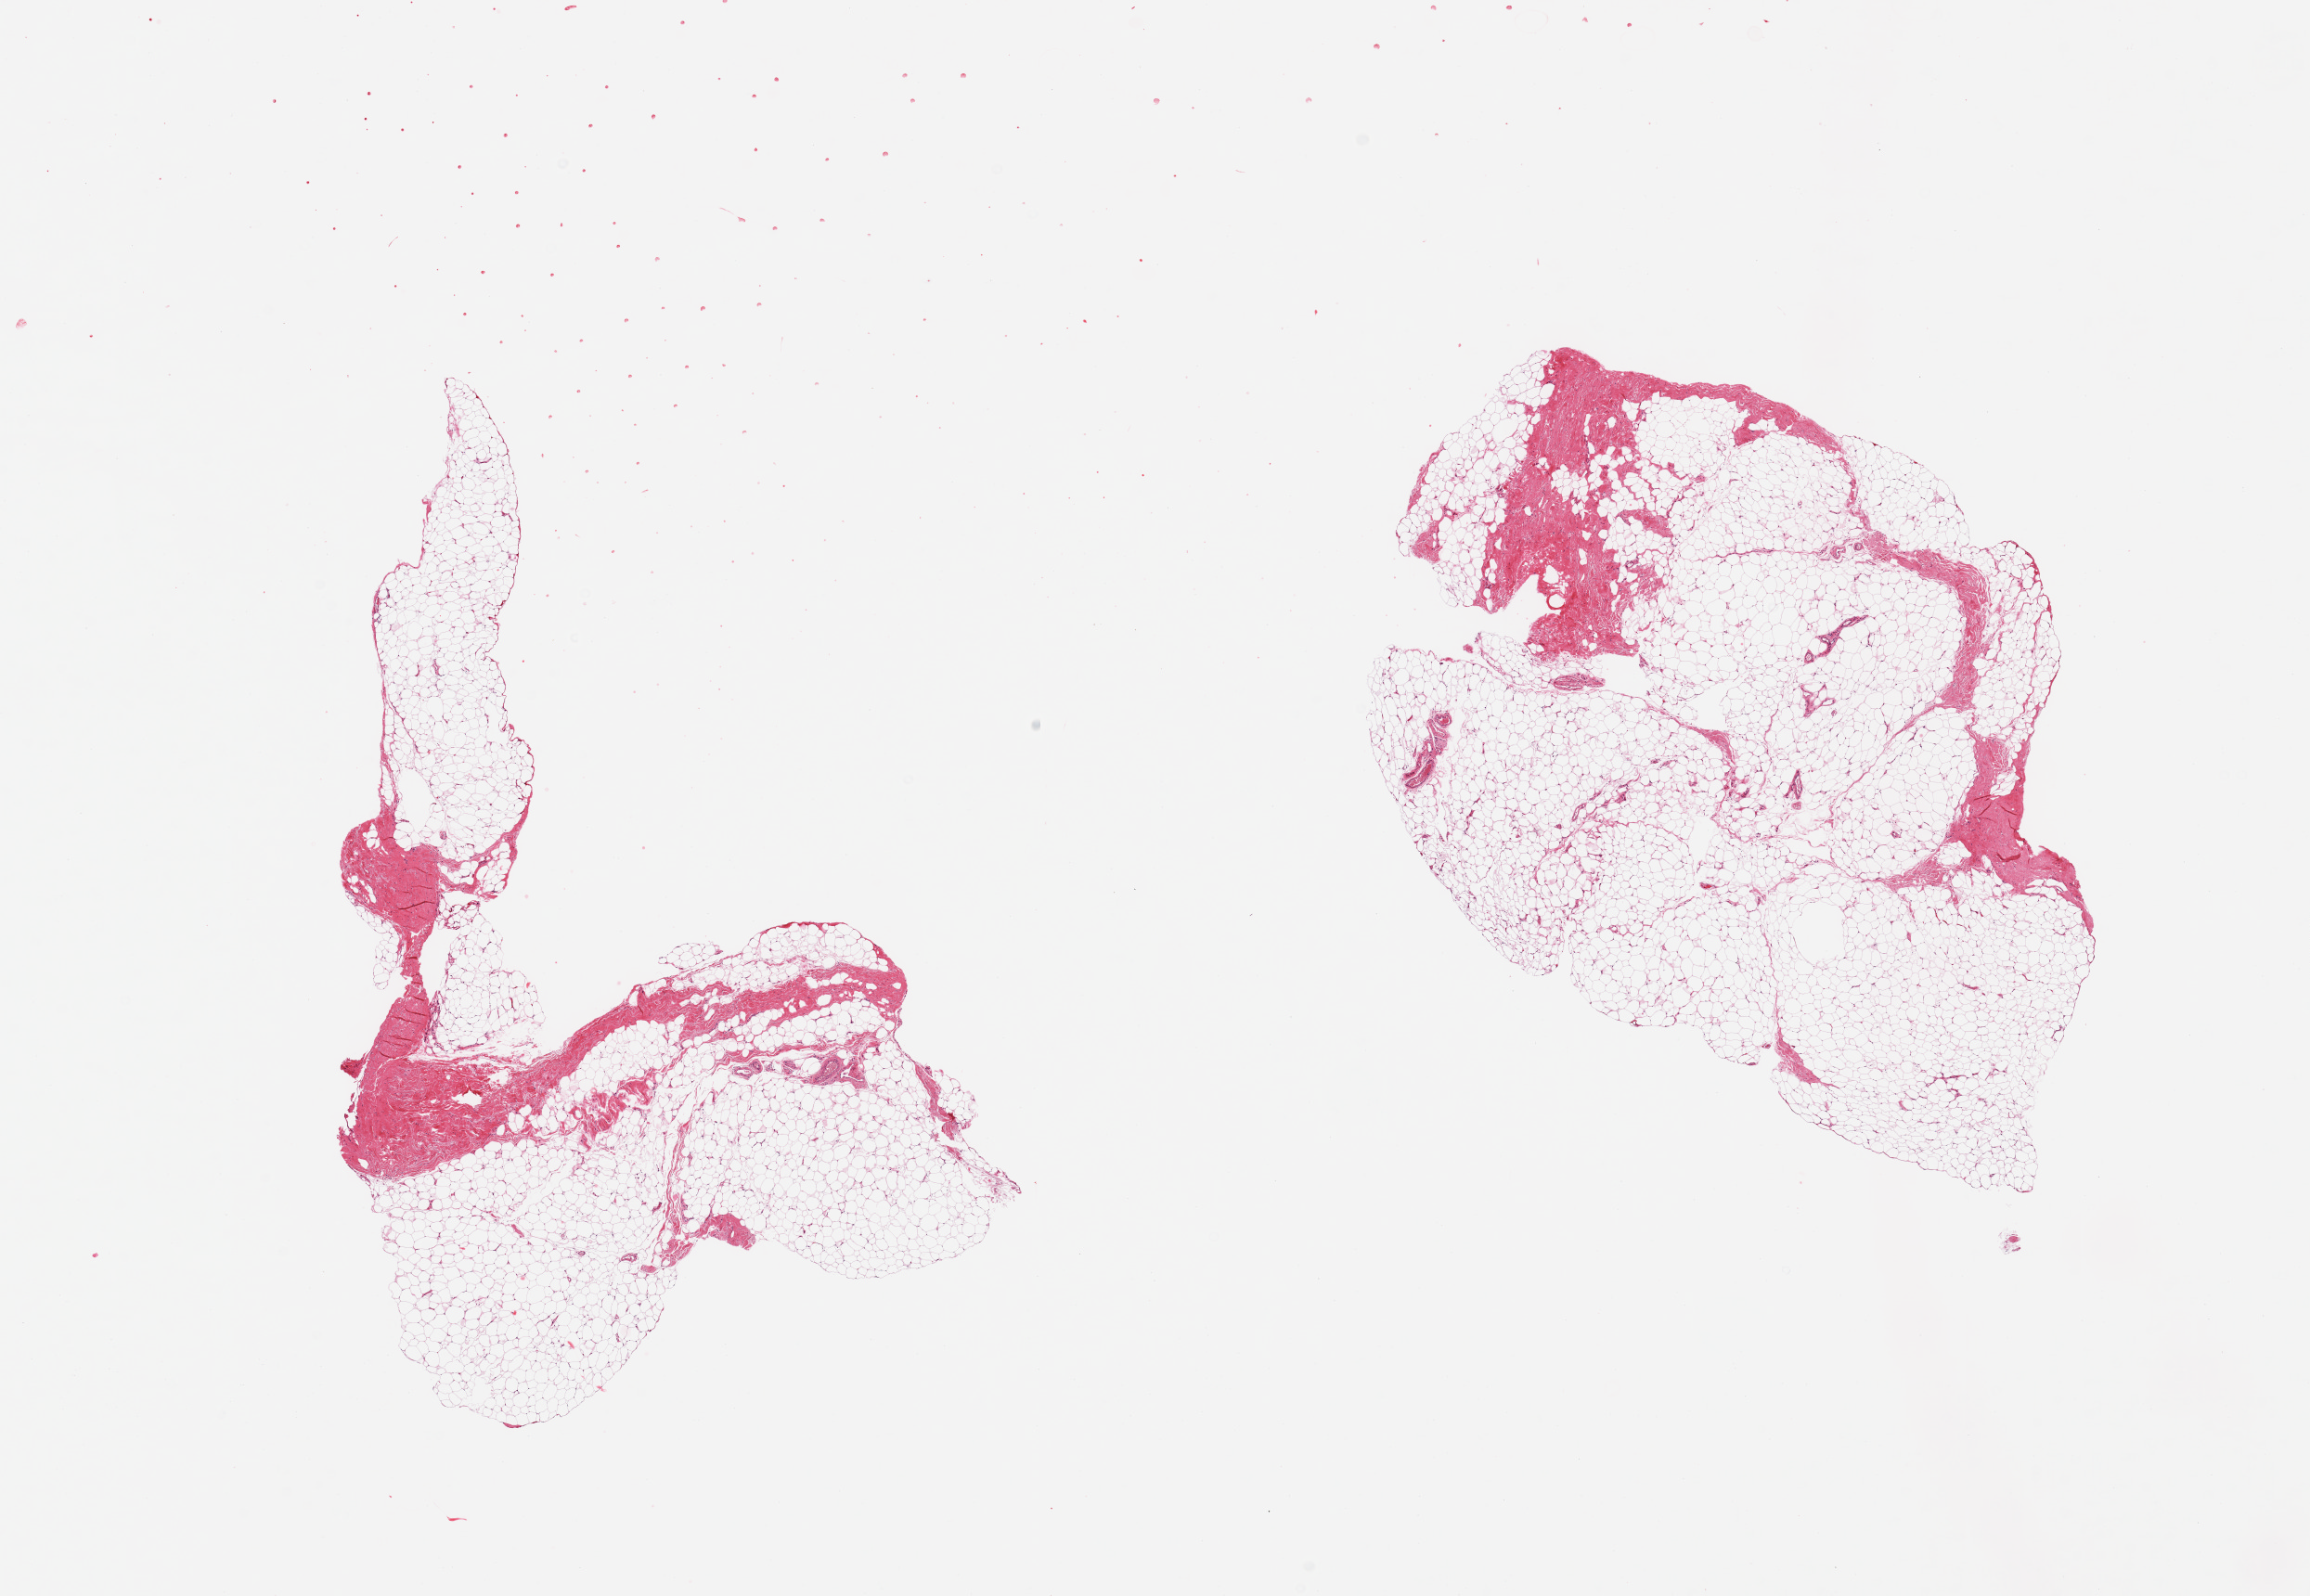
H&E whole-slide image — low-resolution overview of the scanned area, about 19.7 x 13.6 mm; PAXgene-fixed, paraffin-embedded tissue; section of breast (target tissue); tissue donor sample. Donor: female.
Review note (as recorded): 2 pieces; fibrofatty tissue without mammary ducts.